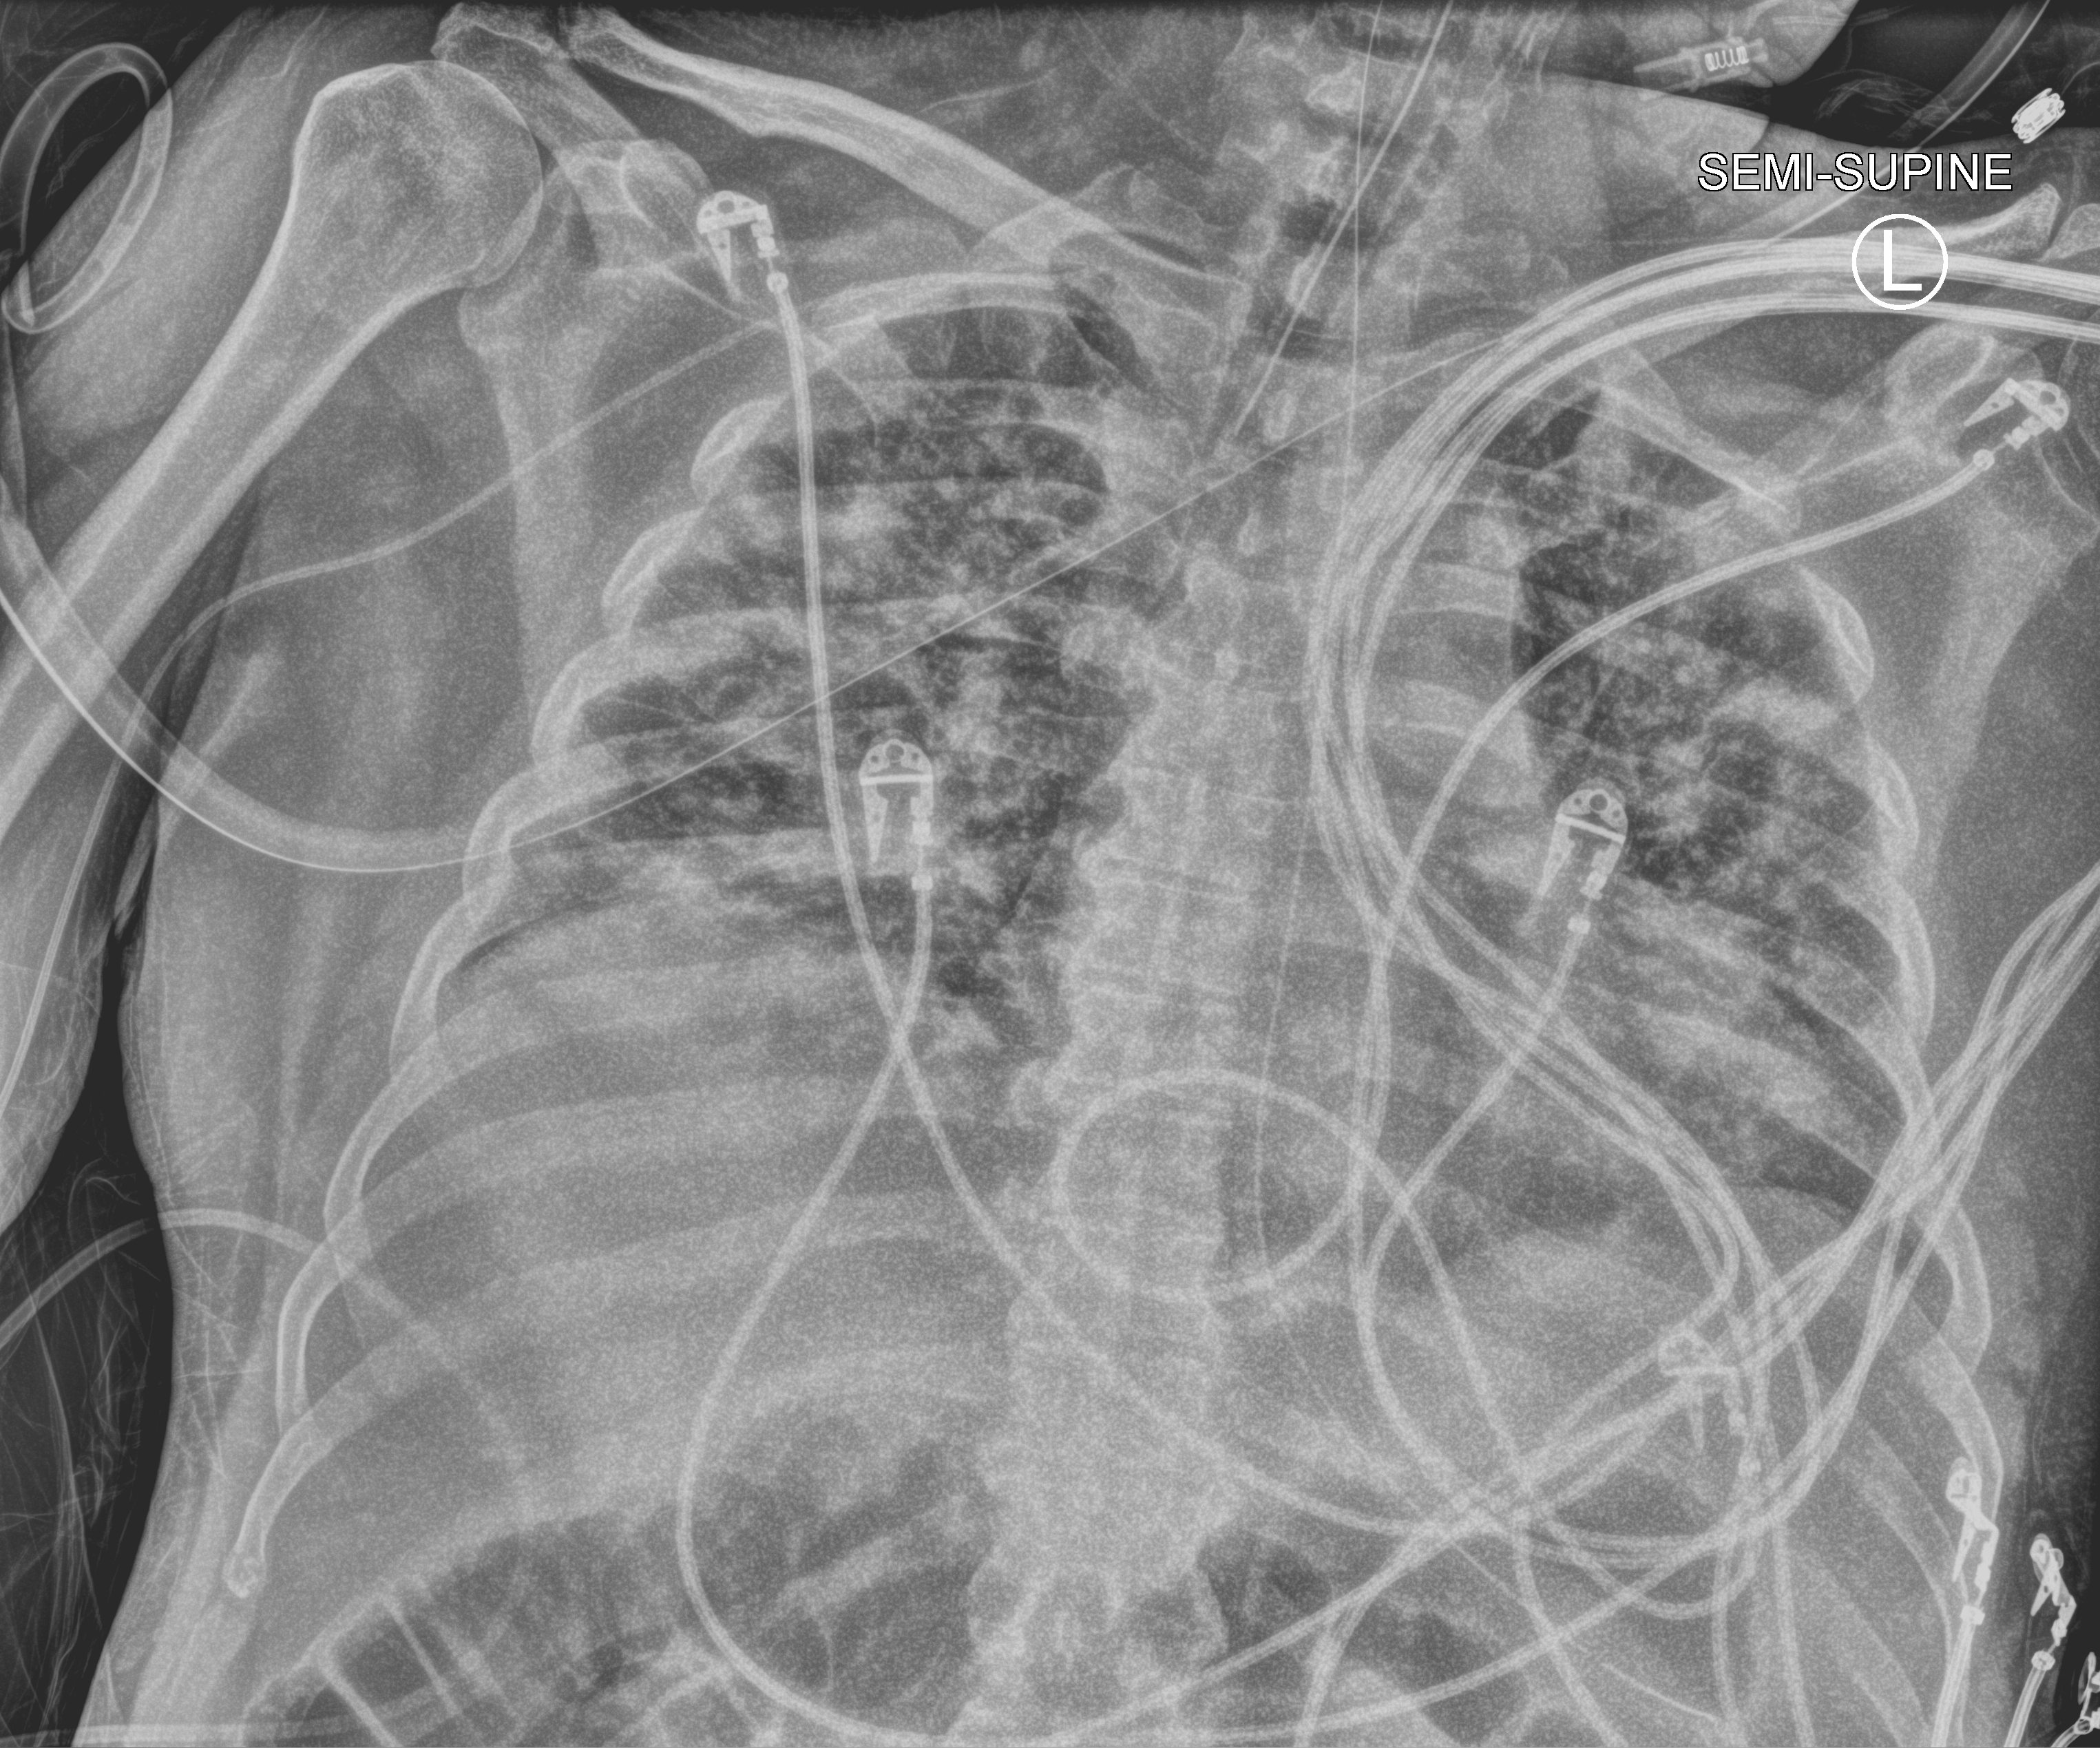
Chest X-ray (portable), anteroposterior (AP) projection. Patient hospitalised with COVID-19; male, aged 18–59 years.
Admission-level facts for this patient (not findings on this image; timing relative to this image not recorded): mechanically ventilated during this hospital stay: yes.